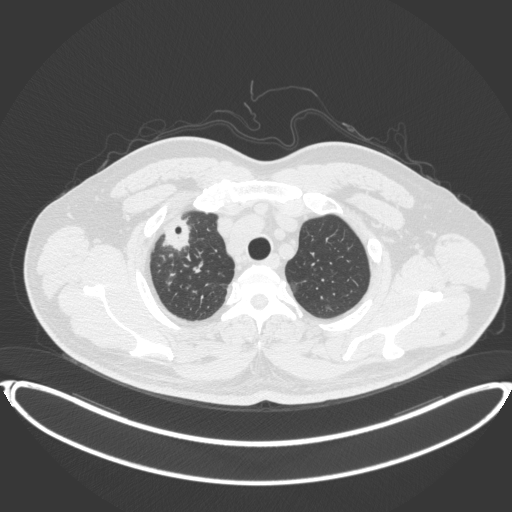
Chest CT, one axial slice; position 333 of 399 along the scan axis; reconstruction kernel B31f; 120 kVp; lung window (W 1500 / L -600 HU); 1 mm slice thickness; 512 × 512 image matrix, field of view 445 × 445 mm. Patient: male, 53 years. Case-level facts recorded for this patient, not image findings: clinical TNM (as recorded): T2a N0 M0.
Outlined on this slice (rectangle marked by the reading radiologist):
- lung tumour (recorded histology: adenocarcinoma): box from (x=160, y=214) to (x=195, y=261) px